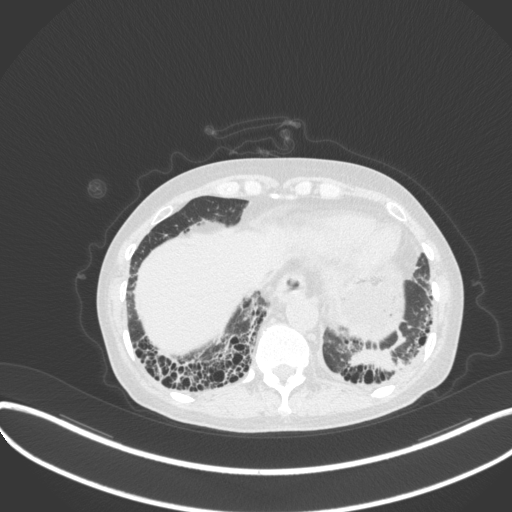
Chest CT, one axial slice. Position 59 of 373 along the scan axis. Reconstruction kernel B31f. 120 kVp. Lung window (W 1500 / L -600 HU). 1 mm slice thickness. 512 × 512 image matrix. Patient: female, 56 years. Case-level facts recorded for this patient, not image findings: clinical TNM (as recorded): T1 N0 M0.
Annotated regions visible in this slice (rectangle marked by the reading radiologist):
- lung tumour (recorded histology: adenocarcinoma): bounding box [x1, y1, x2, y2] px = [340, 346, 408, 377]